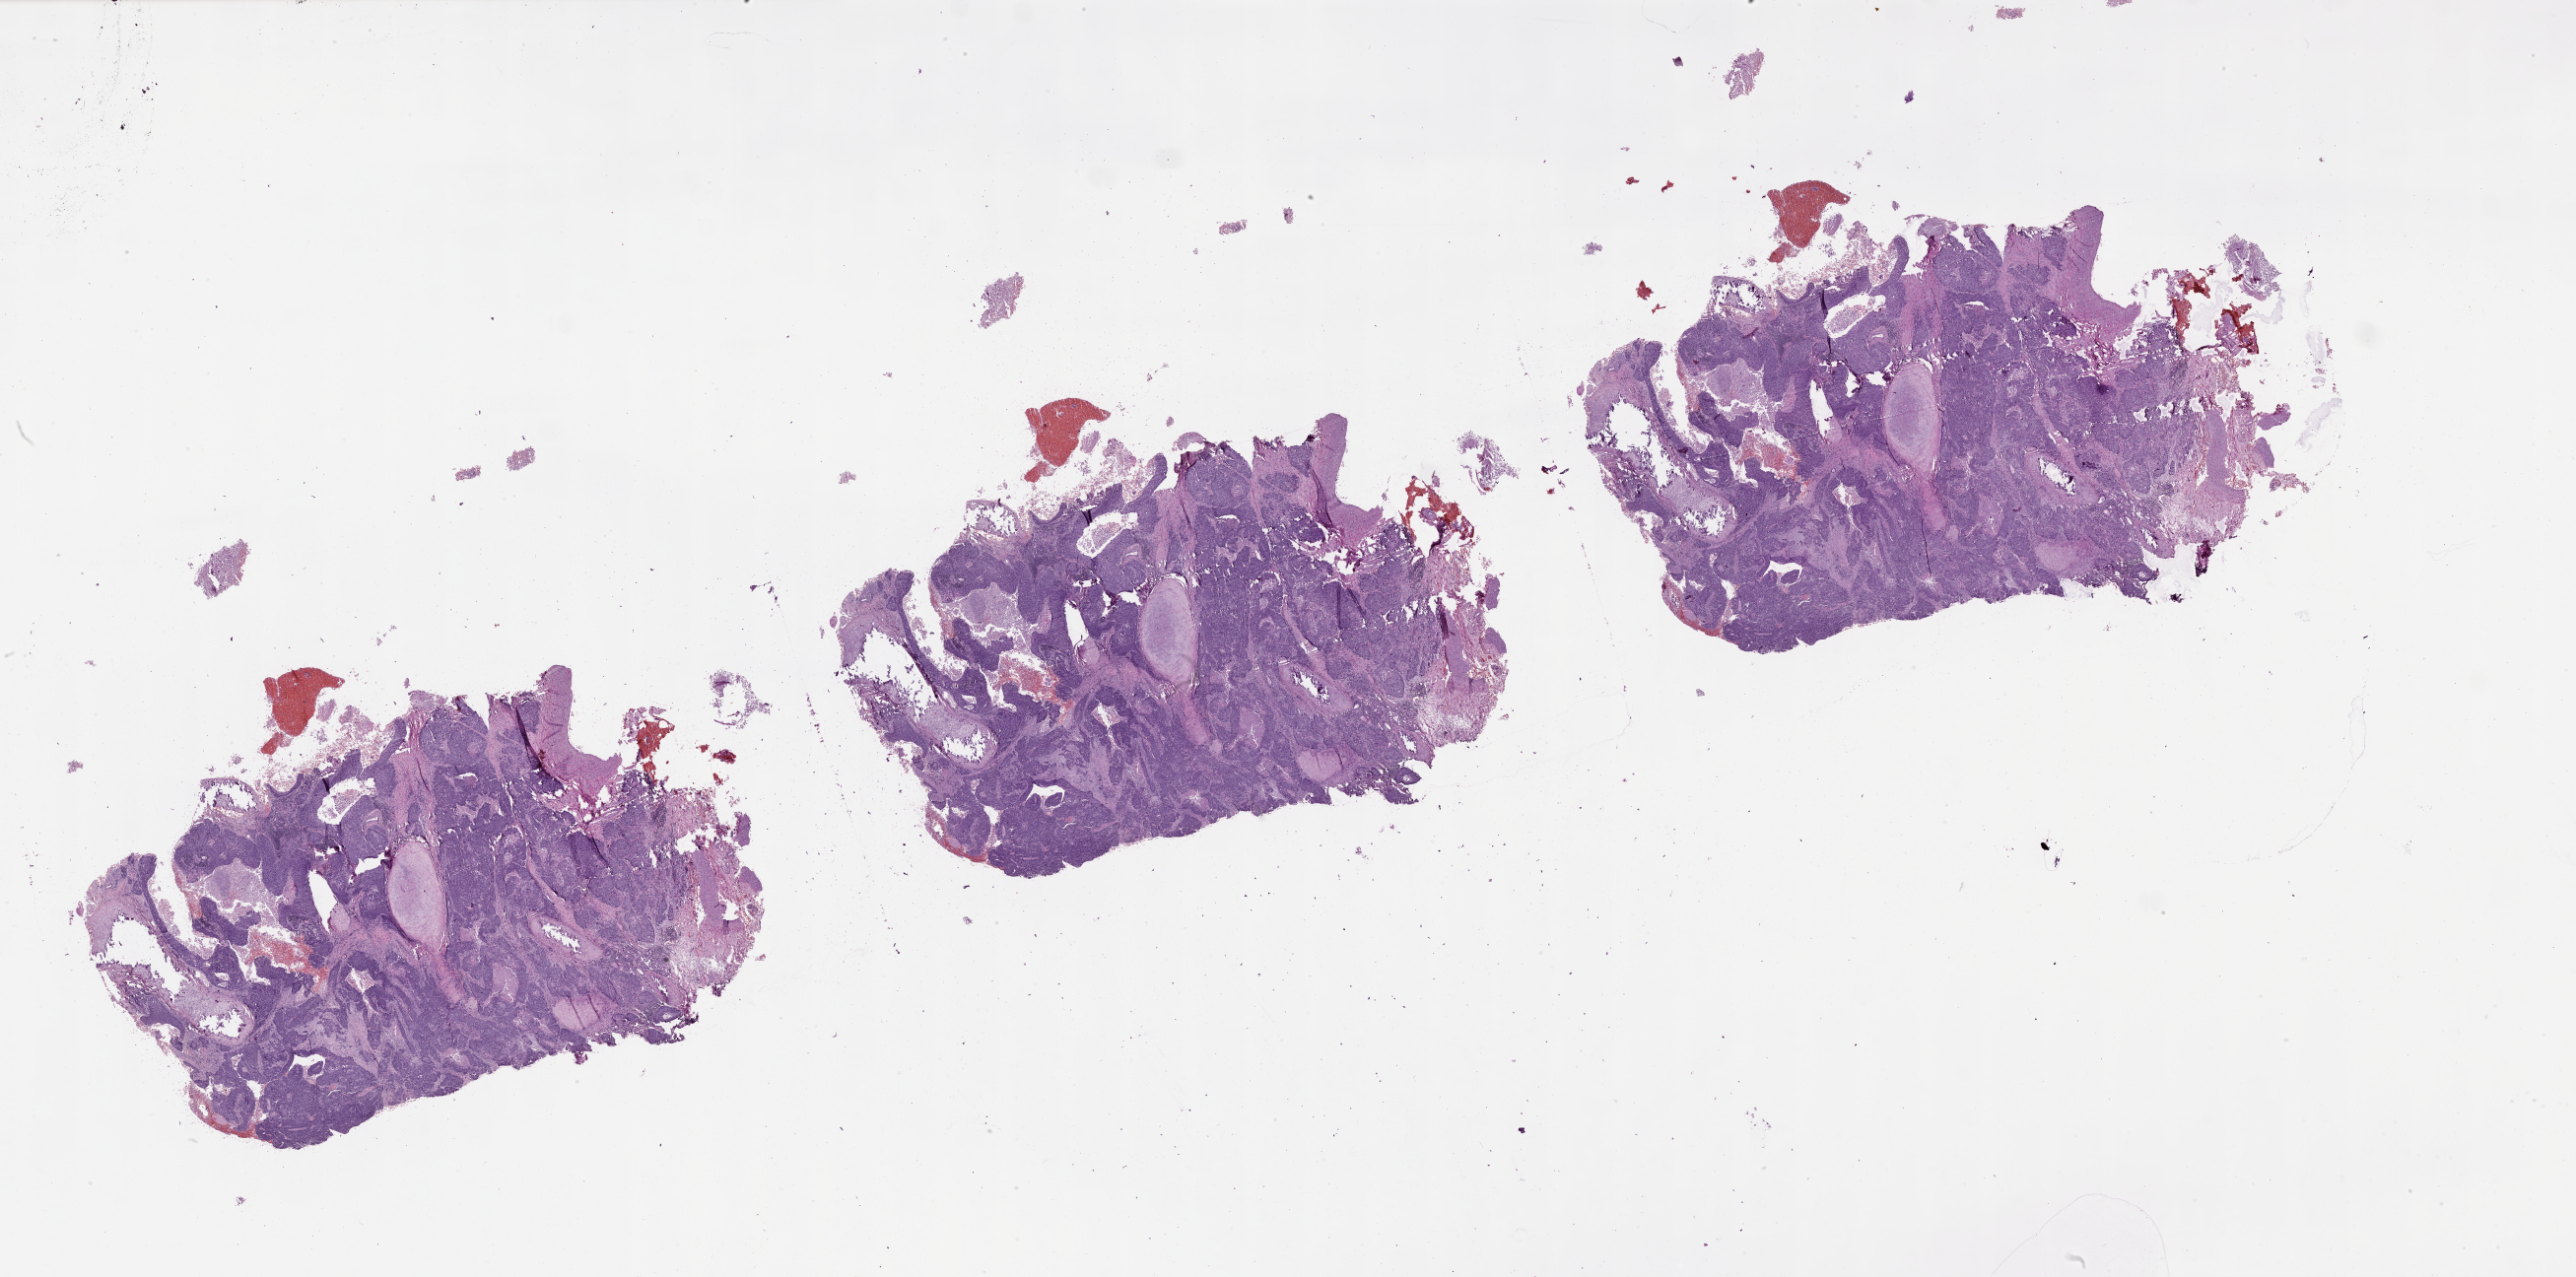
H&E whole-slide image — a low-resolution overview of the entire scanned area, about 42.1 x 20.9 mm; tumour tissue sample, lung. Male, 67 y/o.
- patient diagnosis (cohort enrolment): squamous cell carcinoma (lung)